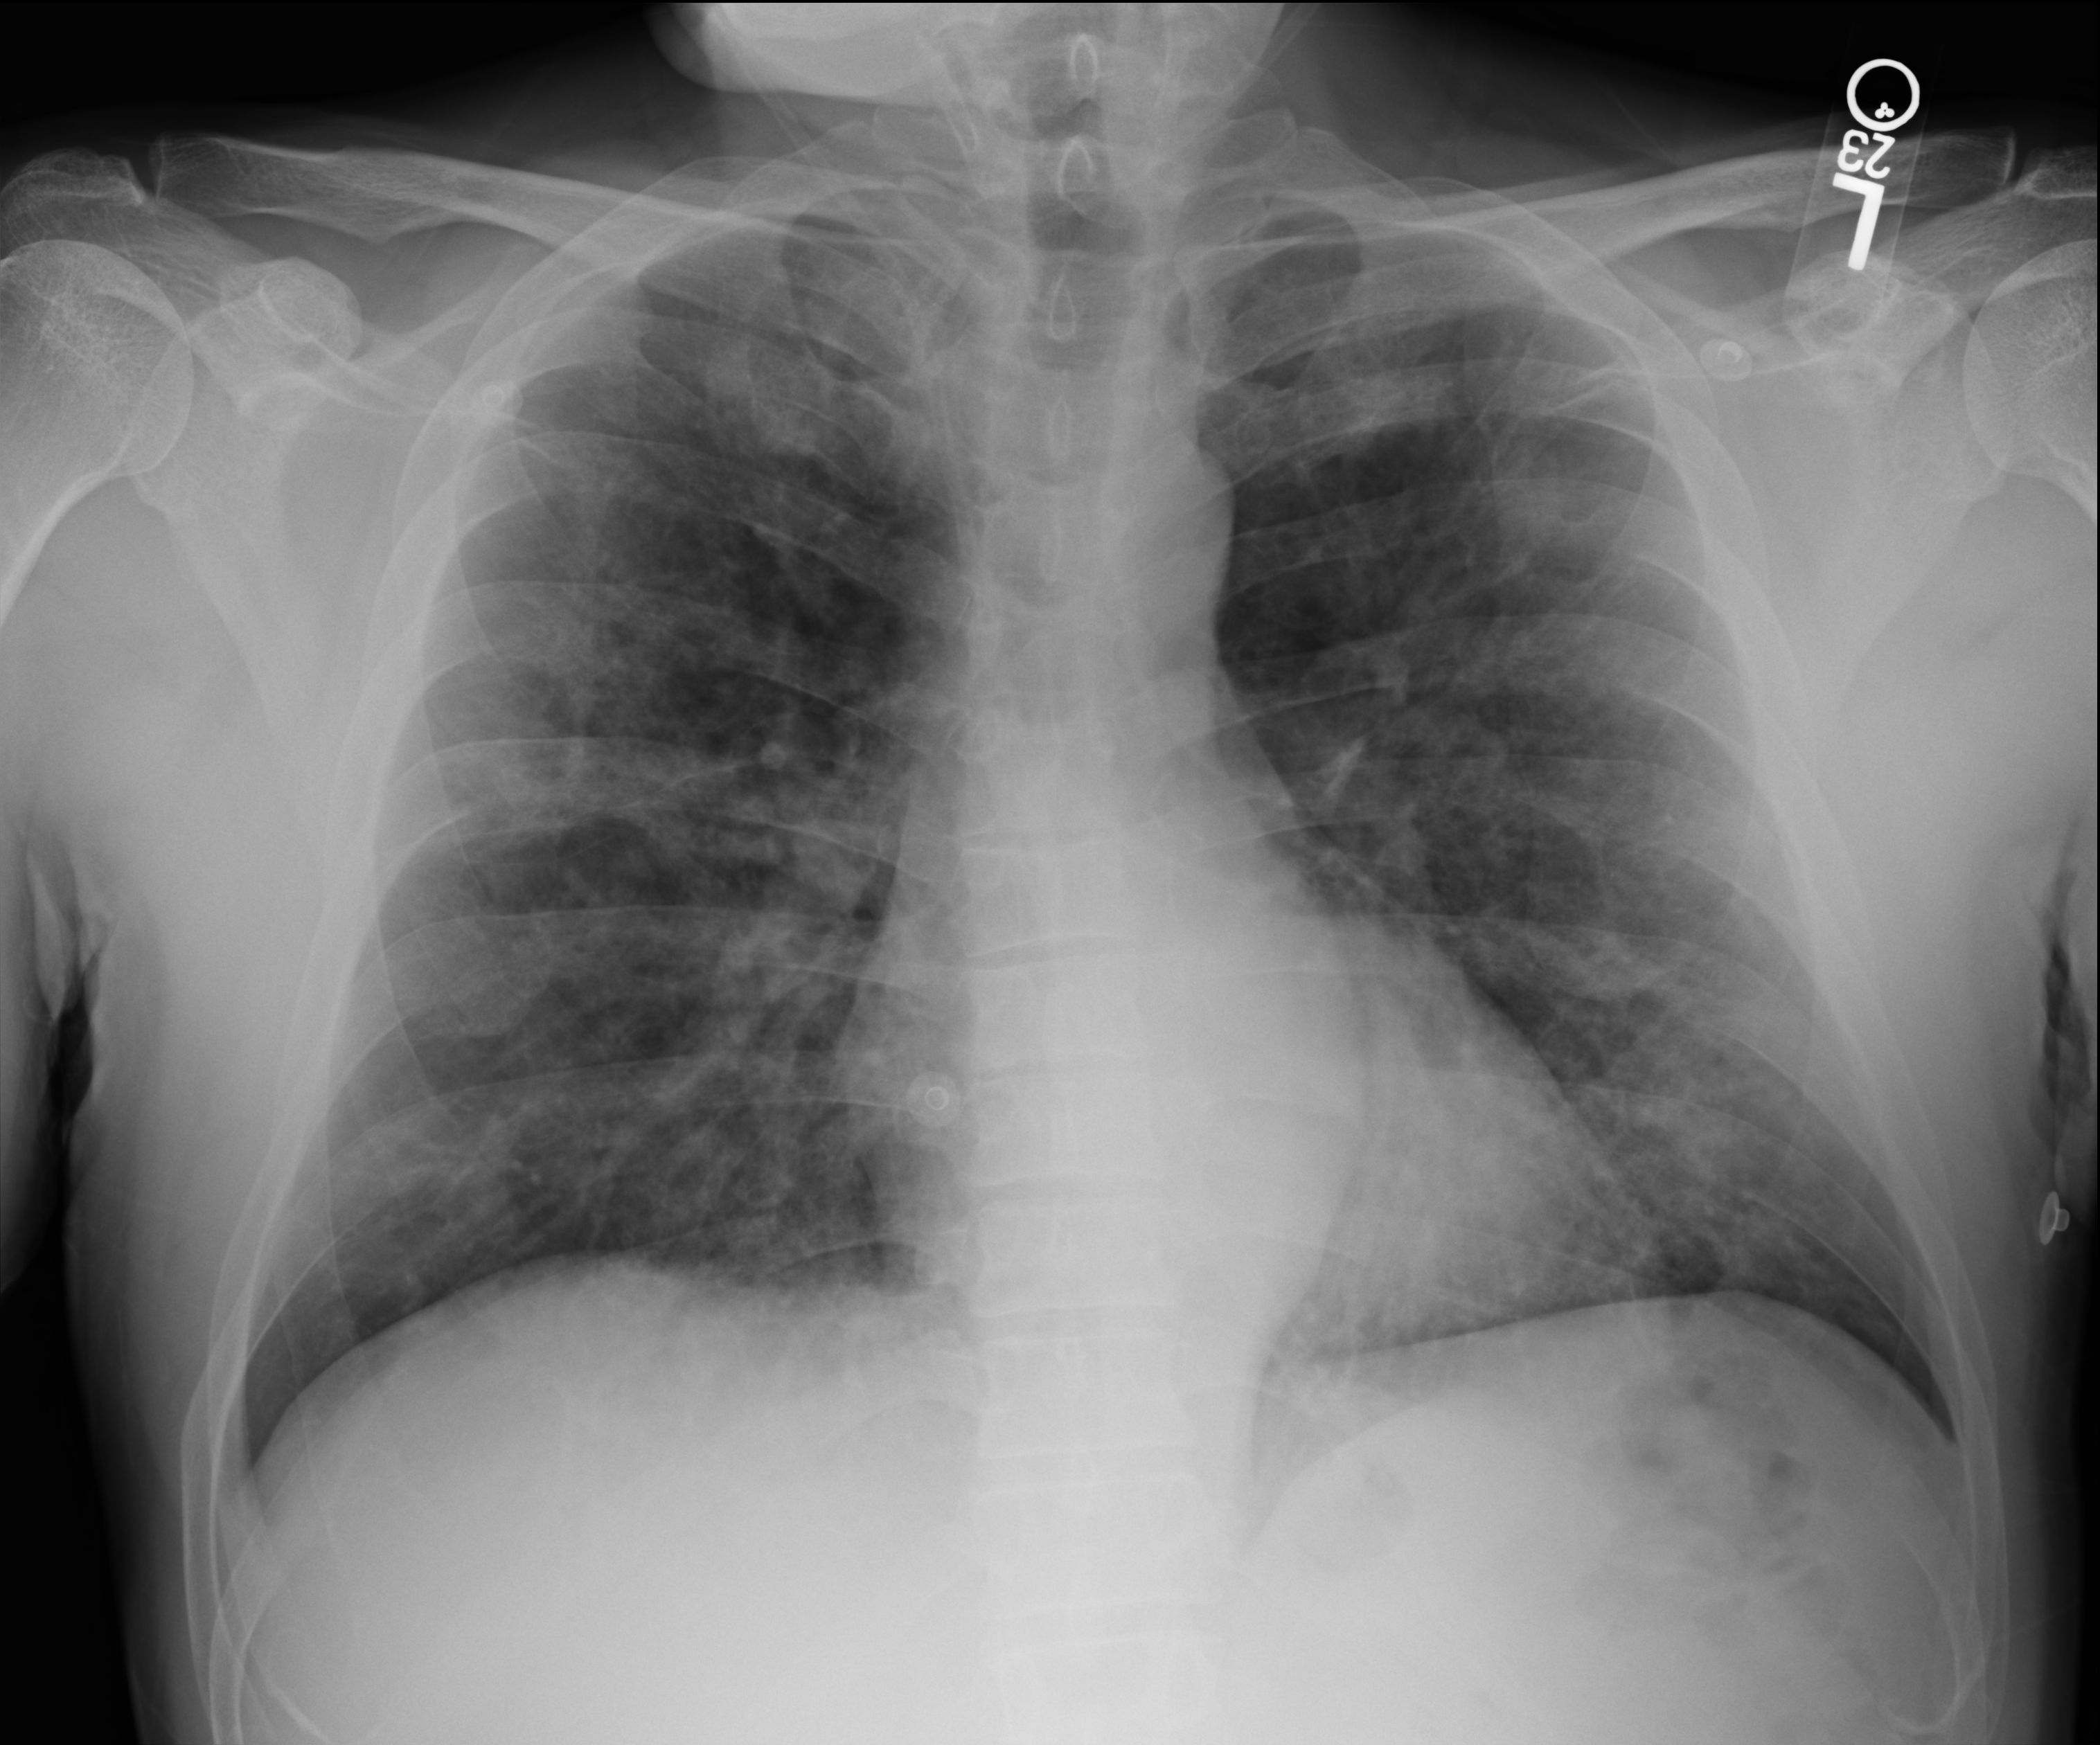
Chest X-ray (portable), anteroposterior (AP) projection. Patient hospitalised with COVID-19; male, aged 18–59 years.
Admission-level facts for this patient (not findings on this image; timing relative to this image not recorded):
- admitted to intensive care during this hospital stay: no